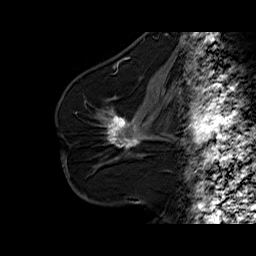
Breast MRI (dynamic contrast-enhanced), one sagittal slice; slice 33 of 60 in the series (ordered by position); dynamic contrast-enhanced series, time point 2 of 6 at this slice position (early post-contrast); 1.5 T; TE 6.3 ms, TR 32.5 ms; 4 mm slice thickness; 256 × 256 image matrix, field of view 200 × 200 mm. Female patient. From the clinical record (not read from this slice): setting: breast cancer imaged before/during neoadjuvant chemotherapy; receptor status: HR-positive, HER2-negative.
Annotated regions visible in this slice (semi-automatic segmentation, software-assisted and operator-edited):
- analysis volume of interest (the breast-tissue region the enhancement analysis was run in; not a lesion): bounding box <95,103,161,164> (left, top, right, bottom; pixels)
- tumour enhancement mask (voxels above the 100 % enhancement threshold inside the analysis volume of interest): <107,112,139,148>